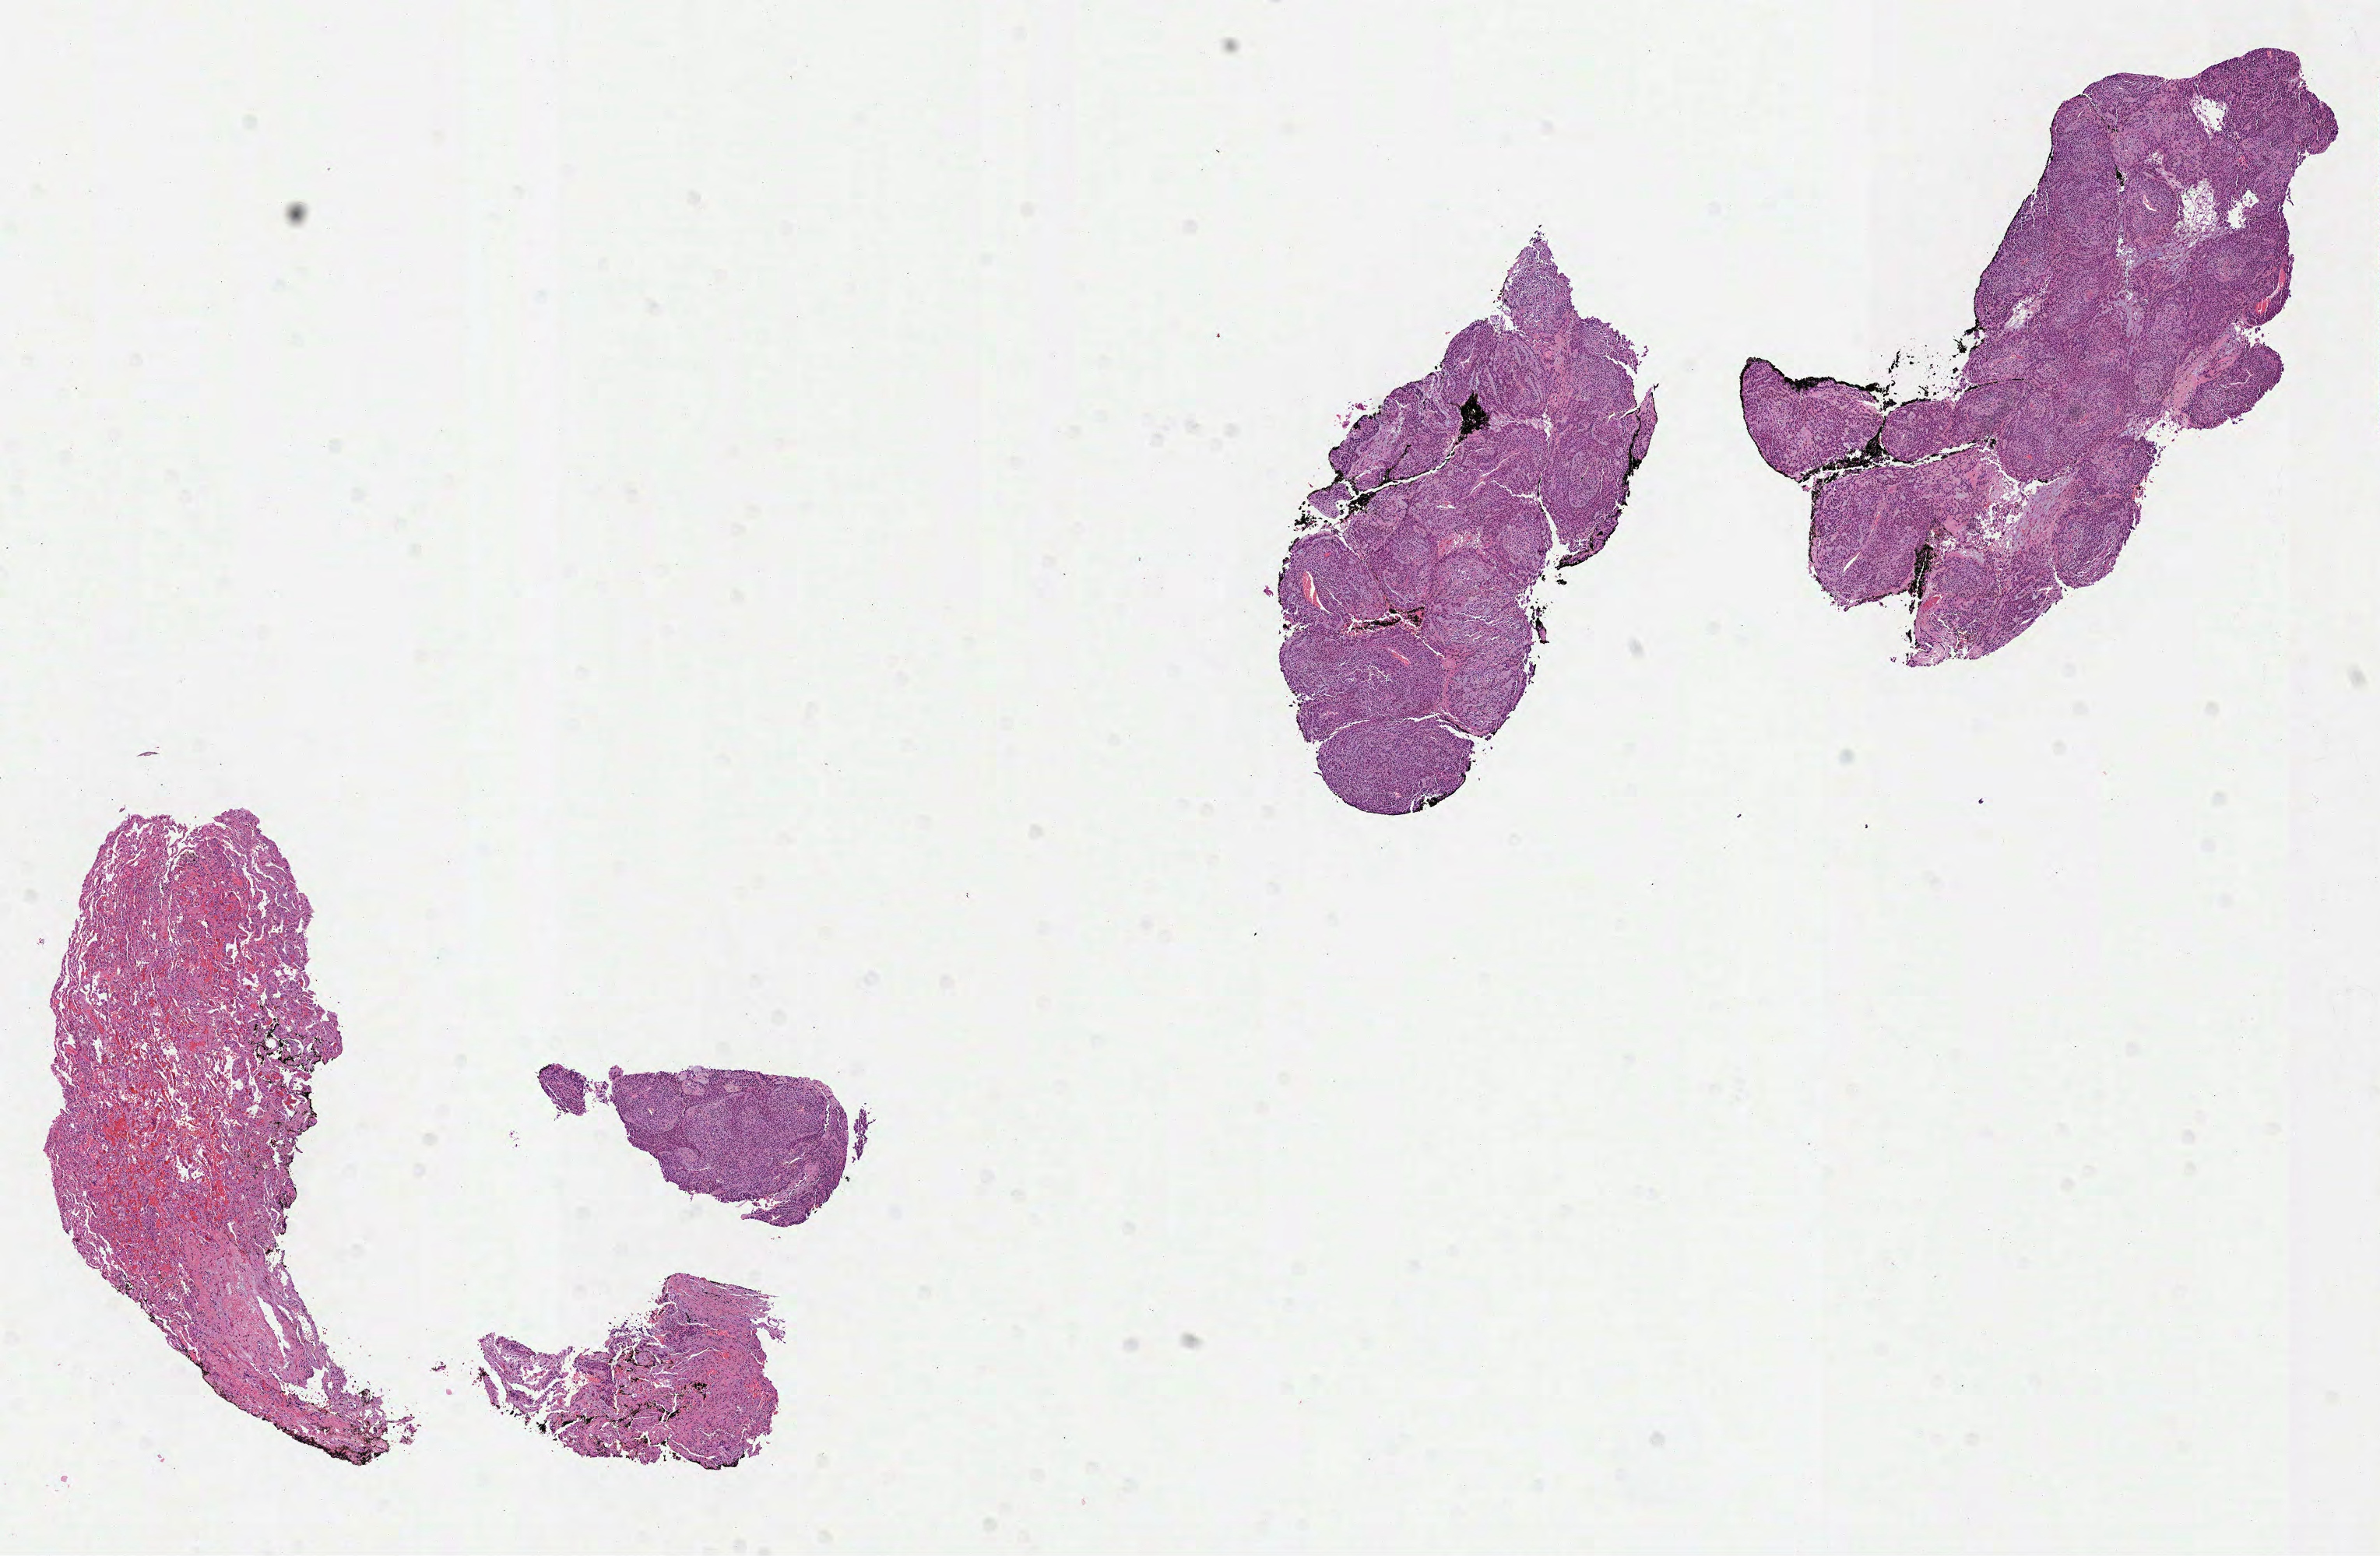
Whole-slide histology image, H&E-stained, low-resolution overview of the scanned area, about 12.3 x 8.1 mm (from a 40x scan); formalin-fixed paraffin-embedded (FFPE) diagnostic section; sample: primary tumour, lung. Male patient; age at initial diagnosis 56 years.
• pathologic diagnosis: Squamous cell carcinoma, NOS
• AJCC pathologic stage: IB (7th edition)